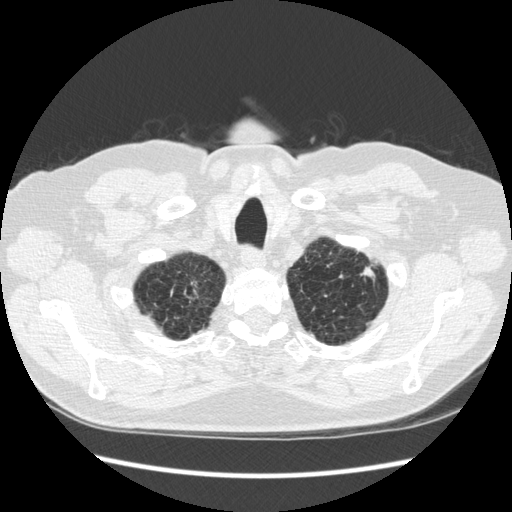
Low-dose screening chest CT, one axial slice. Position 245 of 267 along the scan axis. Lung window (W 1500 / L -600 HU). 512 × 512 image matrix.
Outlined on this slice (manually delineated by an expert):
- lesion 1 (tumor, upper lobe of left lung): bounding box <361,268,375,277> (left, top, right, bottom; pixels)